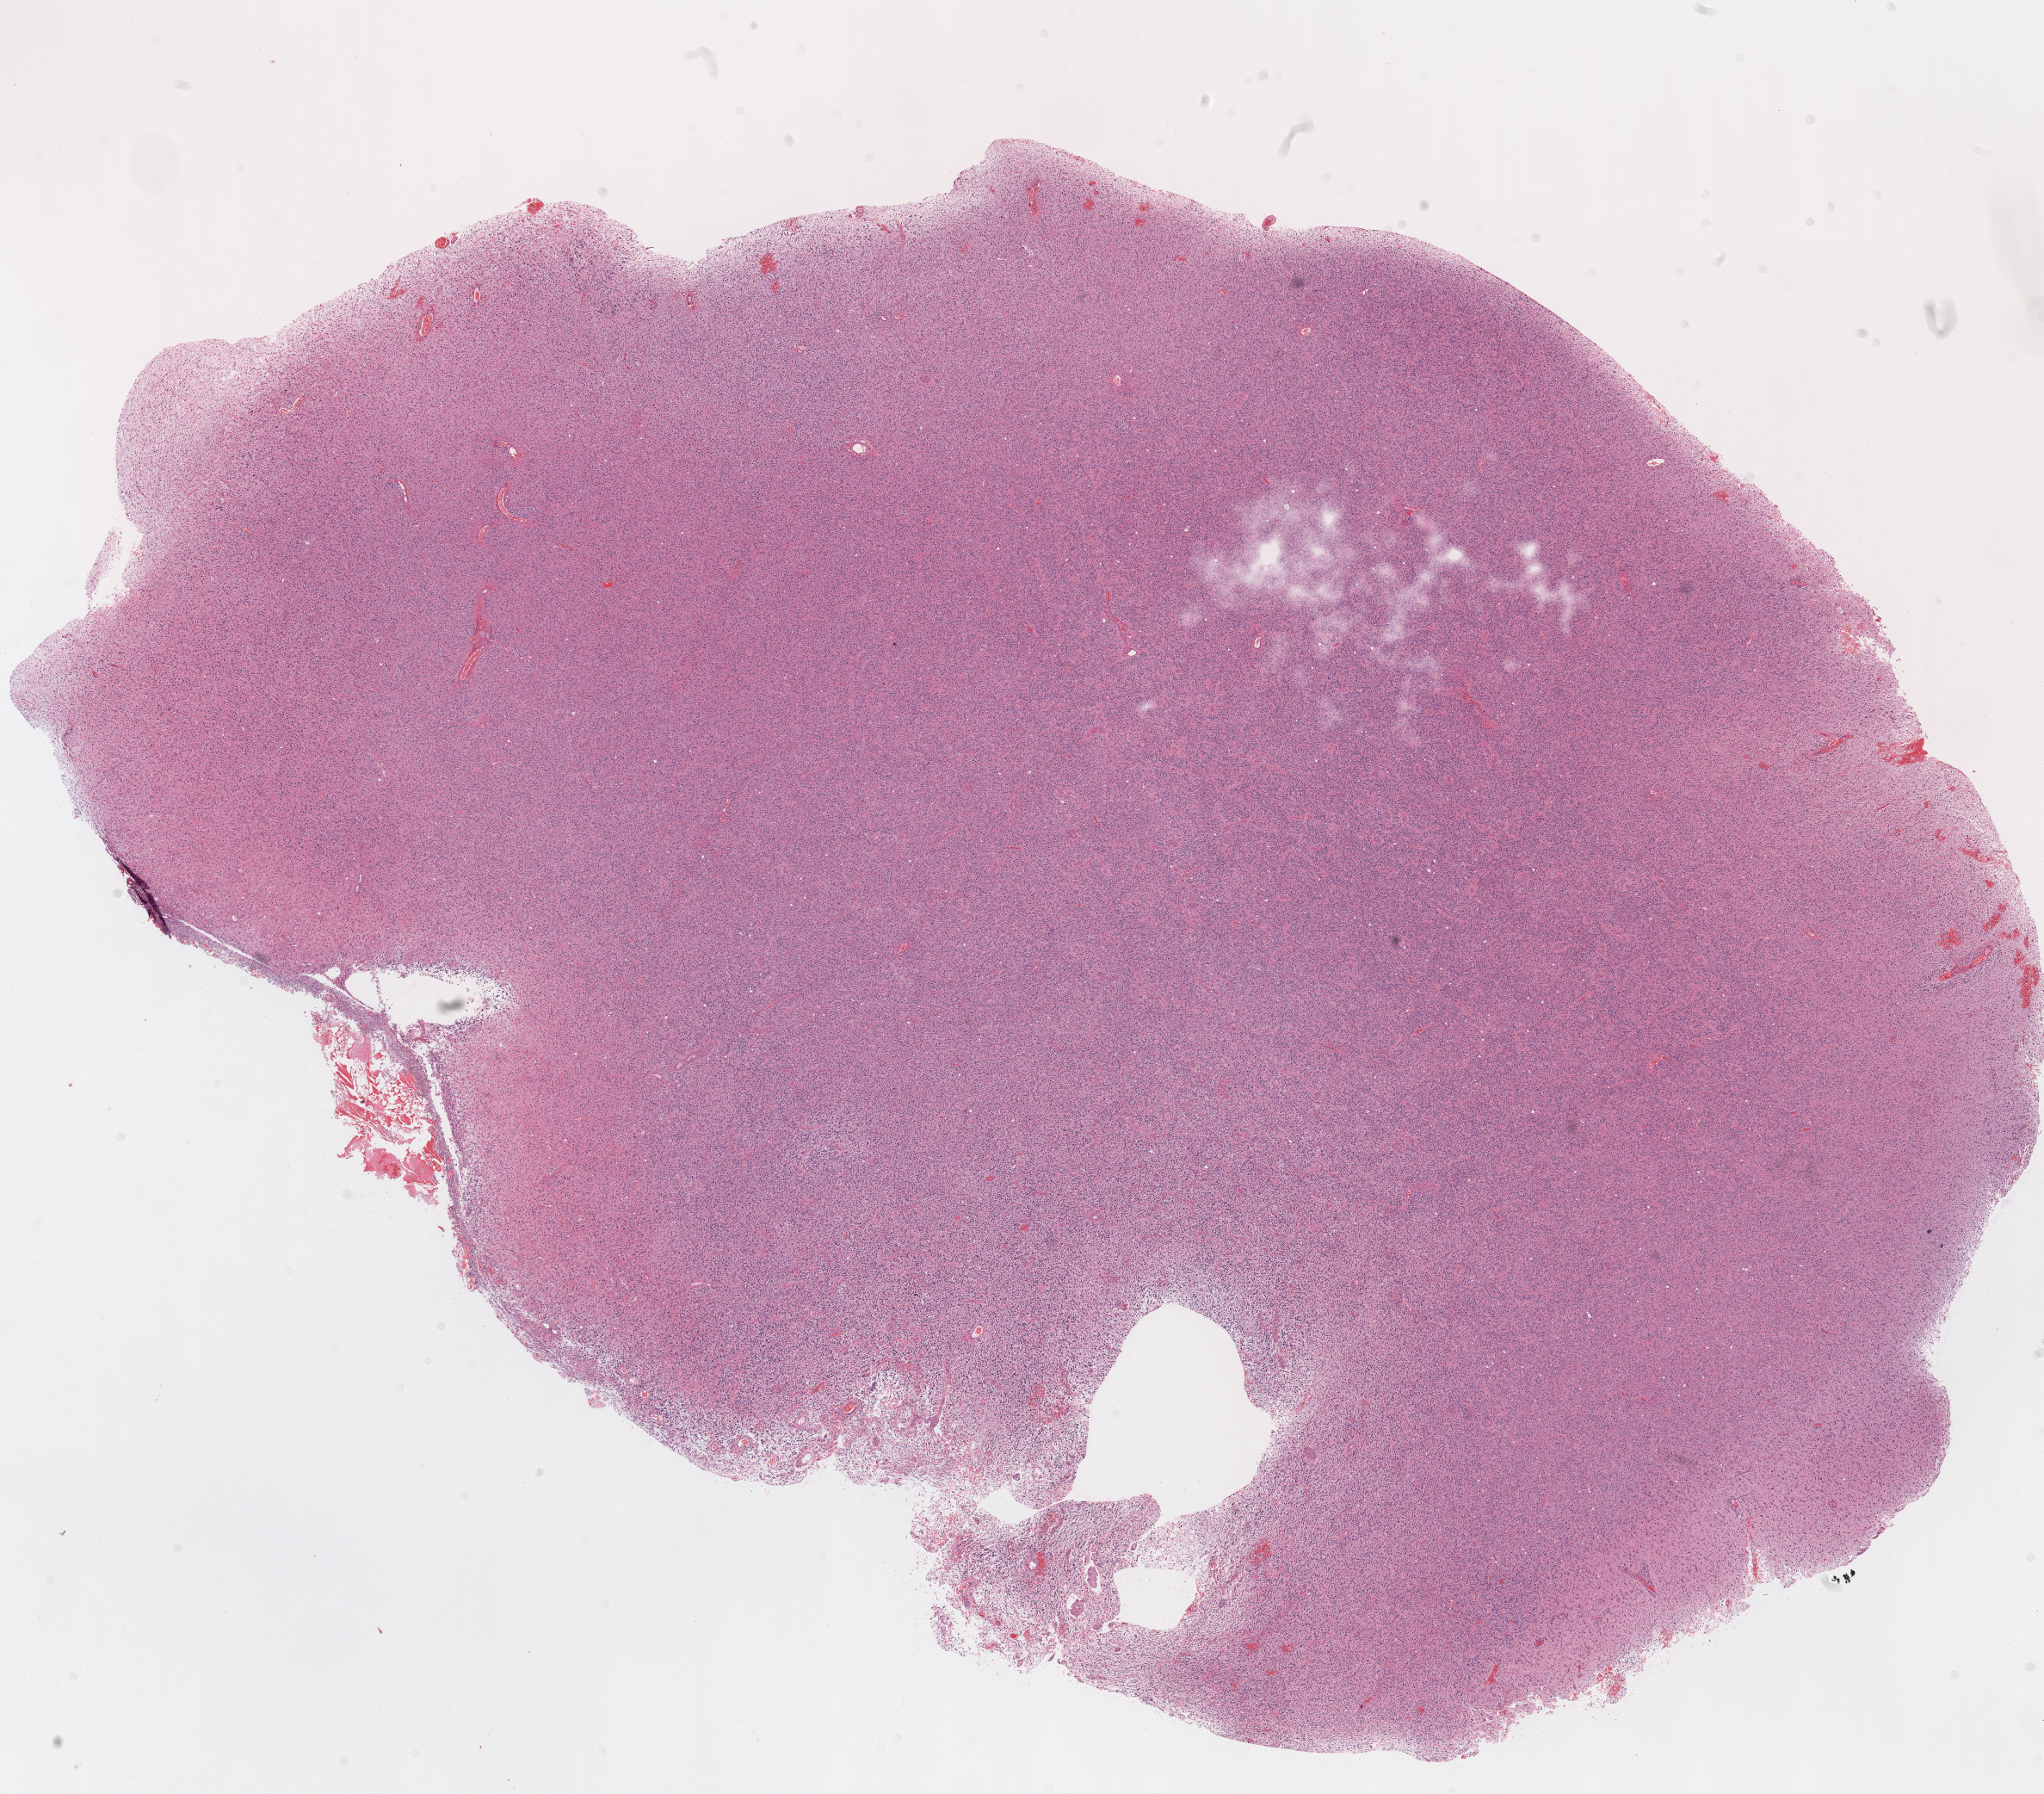
Digitized H&E-stained tissue section (whole slide) — a low-resolution overview of the entire scanned area, about 19.1 x 16.7 mm, formalin-fixed paraffin-embedded (FFPE) diagnostic section, brain, primary tumour sample. Male patient; age at initial diagnosis 38 years.
• pathologic diagnosis: Glioblastoma